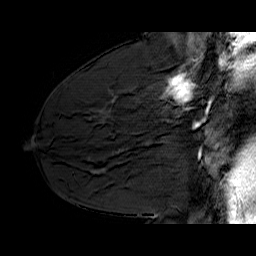
Breast MRI (dynamic contrast-enhanced), one sagittal slice; dynamic contrast-enhanced series, time point 2 of 6 at this slice position (early post-contrast); 1.5 T; TE 6.4 ms, TR 32.9 ms; 4 mm slice thickness; 256 × 256 image matrix, field of view 200 × 200 mm. Female patient. From the clinical record (not read from this slice): setting: breast cancer imaged before/during neoadjuvant chemotherapy; receptor status: HER2-positive.
Outlined on this slice (semi-automatically segmented with operator editing):
- analysis volume of interest (the breast-tissue region the enhancement analysis was run in; not a lesion): bounding box <130,62,210,128> (left, top, right, bottom; pixels)
- tumour enhancement mask (voxels above the 100 % enhancement threshold inside the analysis volume of interest): <164,64,196,125>